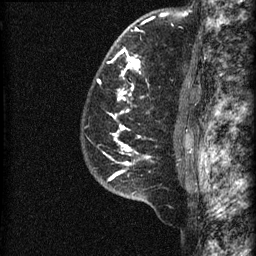
Breast MRI (dynamic contrast-enhanced), one sagittal slice. Slice 49 of 60 in the series (ordered by position). Dynamic contrast-enhanced series, image 2 of 3 at this slice position (ordered by acquisition). 1.5 T. TE 4.2 ms, TR 22.7 ms. 1.5 mm slice thickness. 256 × 256 image matrix, field of view 180 × 180 mm. Patient: female, 48 years. From the clinical record (not read from this slice): setting: breast cancer imaged before/during neoadjuvant chemotherapy; receptor status: triple-negative.
Outlined on this slice (semi-automatically segmented with operator editing):
- analysis volume of interest (the breast-tissue region the enhancement analysis was run in; not a lesion): bounding box [x1, y1, x2, y2] px = [81, 23, 186, 202]
- tumour enhancement mask (voxels above the 90 % enhancement threshold inside the analysis volume of interest): [98, 29, 149, 181]